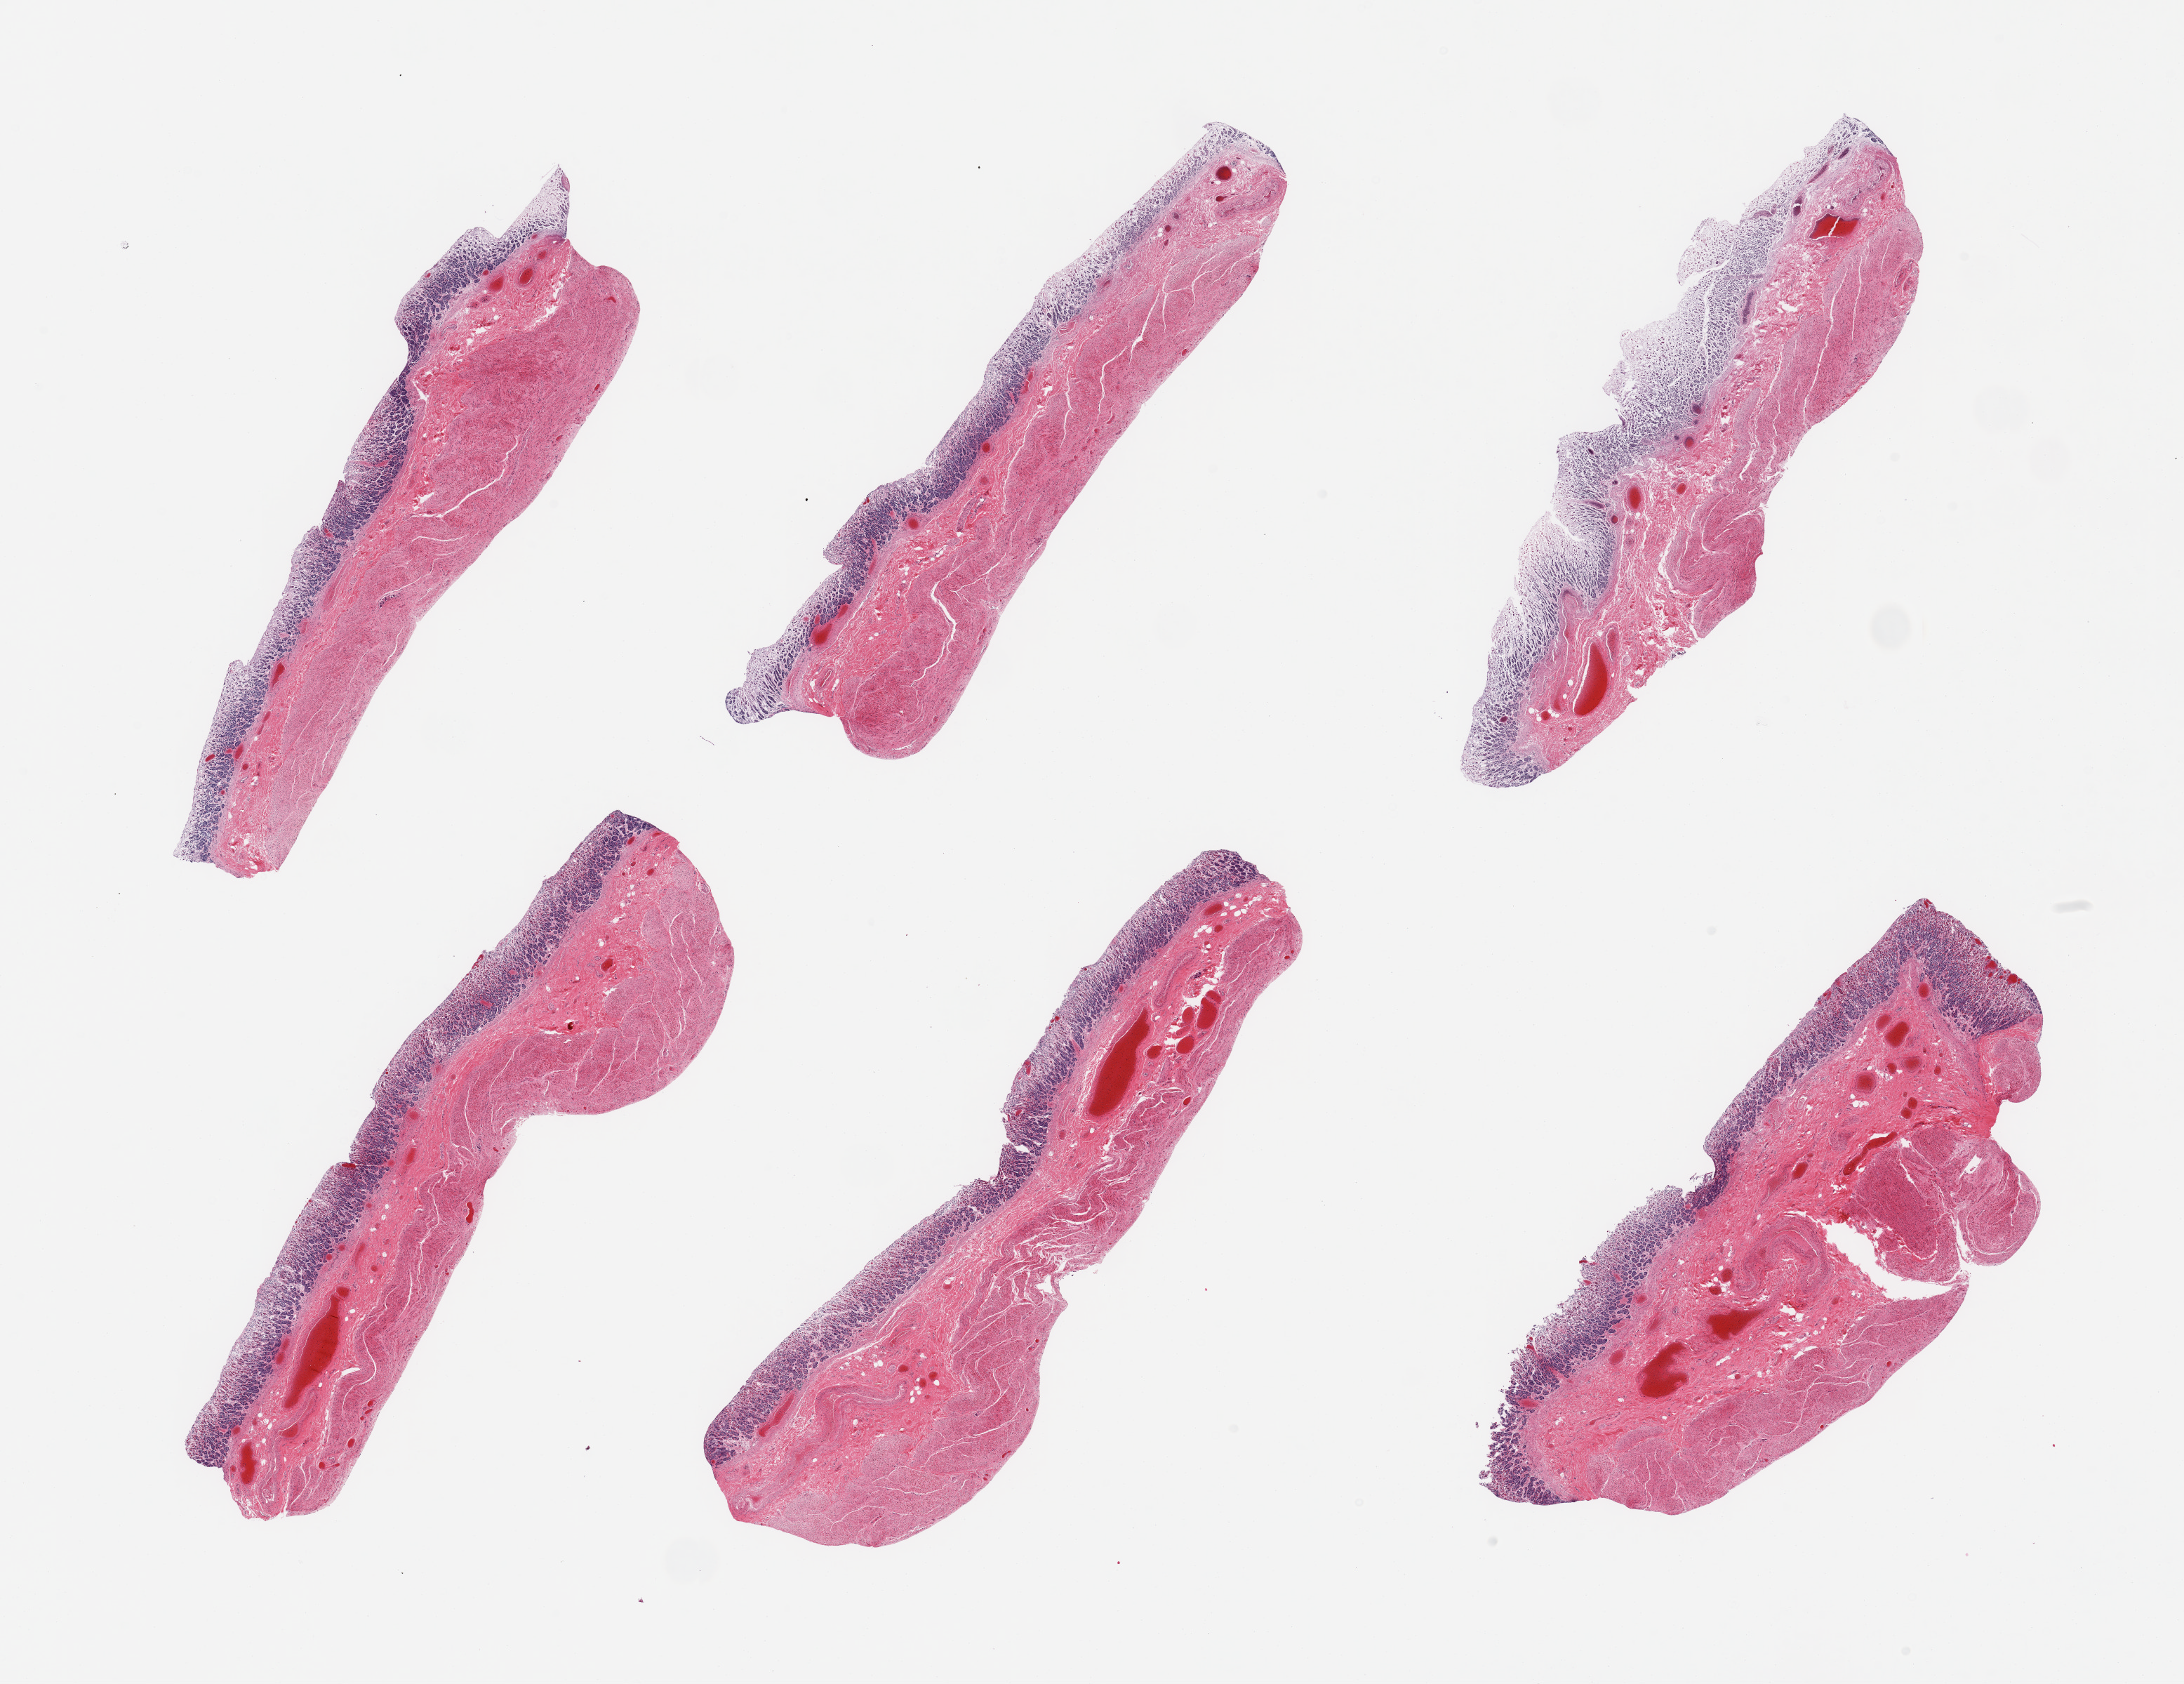
Digitized hematoxylin and eosin (H&E)-stained section, brightfield, shown as a low-resolution overview of the whole scanned area (about 24.6 x 19.0 mm, acquisition: 20x scan). PAXgene-fixed, paraffin-embedded tissue. Target tissue: stomach. Tissue donor sample. Male donor.
Reviewer comment on this tissue sample: 6 pieces, target mucosa up to ~0.8mm, ~40% thickness, advanced autolysis.